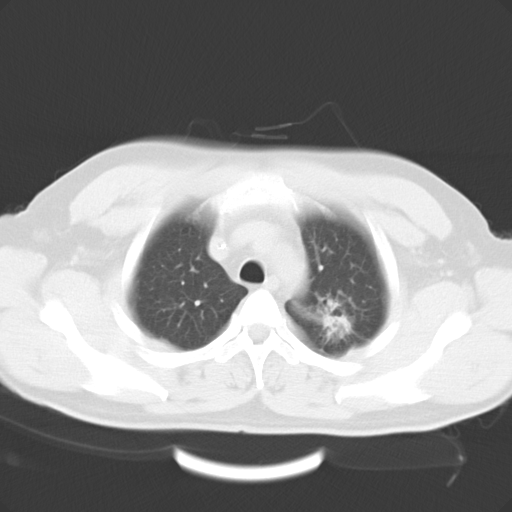
Chest CT, one axial slice; position 16 of 20 along the scan axis; 120 kVp; lung window (W 1500 / L -600 HU); 512 × 512 image matrix, field of view 362 × 362 mm. Male patient, age 45 years. Case-level facts recorded for this patient, not image findings: clinical TNM (as recorded): T2 N0 M0.
Annotated regions visible in this slice (rectangle marked by the reading radiologist):
- lung tumour (recorded histology: adenocarcinoma): box from (x=295, y=286) to (x=374, y=352) px